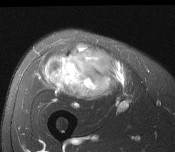
MRI of an extremity soft-tissue mass, one axial slice; slice 78 of 116 in the series (ordered by position); T2-weighted fat-saturated; MR volume resampled by the dataset authors to the PET/CT grid (not the native acquisition matrix); 175 × 152 image matrix, field of view 171 × 148 mm. Male patient. From the clinical record (not read from this slice): histological type: pleiomorphic leiomyosarcoma; grade: intermediate; site of the primary tumour: right thigh.
Outlined on this slice (expert contour drawn on MRI and transferred to this co-registered scan by the dataset authors):
- gross tumour volume including surrounding oedema: bounding box <45,47,116,100> (left, top, right, bottom; pixels)
- gross tumour volume (mass): <45,47,116,100>